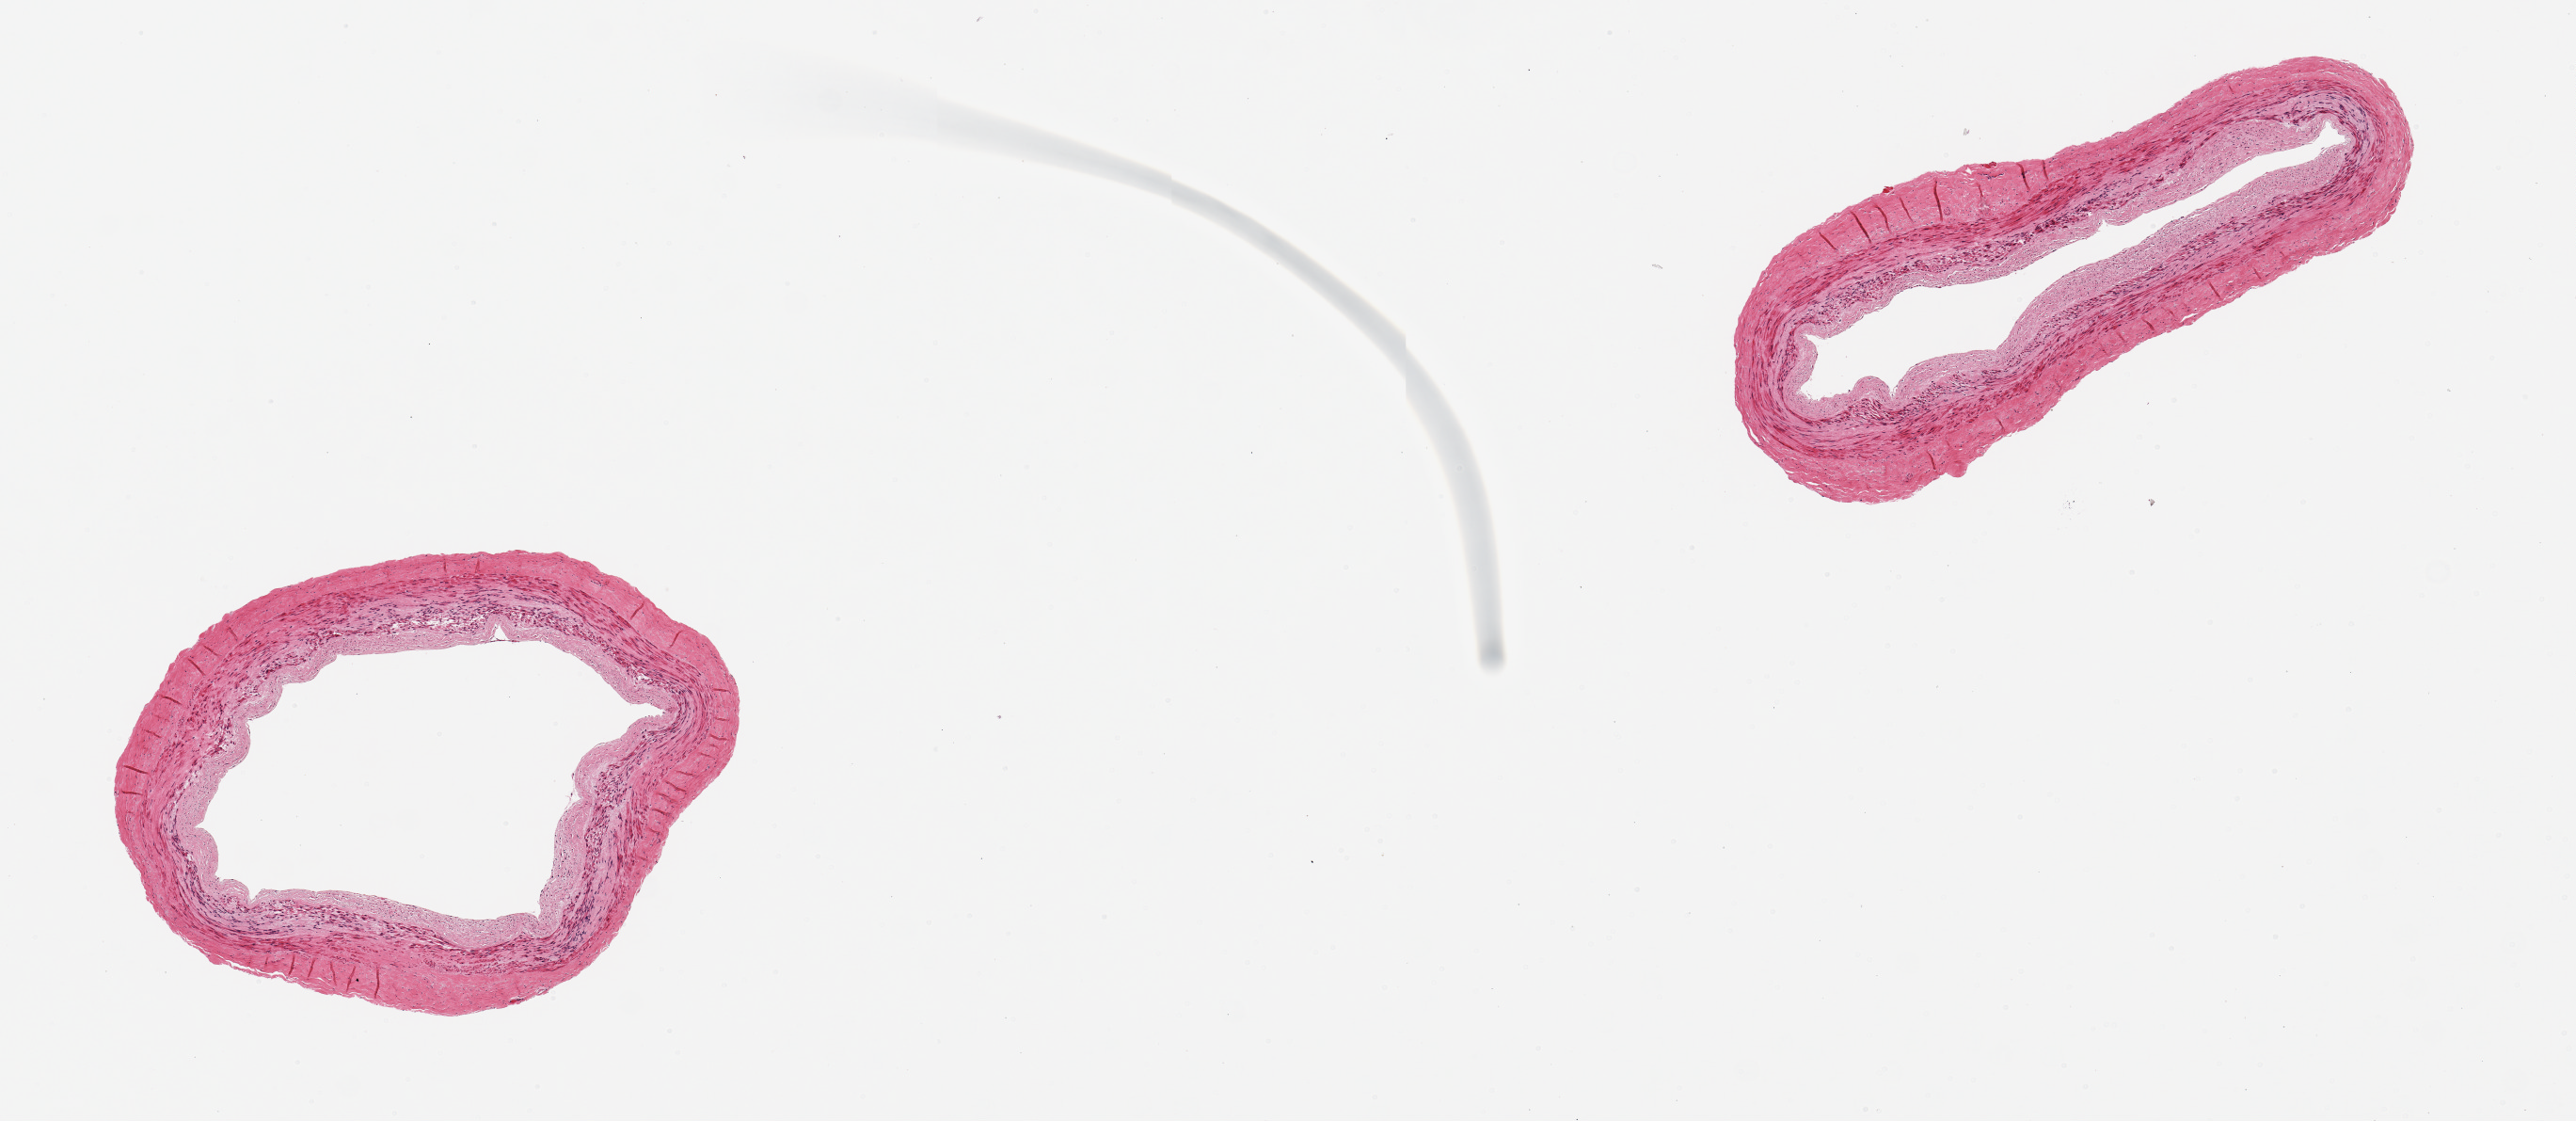
Whole-slide image, haematoxylin and eosin stain — a low-resolution overview of the entire scanned area, about 10.8 x 4.7 mm (slide scanned at 20x), PAXgene-fixed, paraffin-embedded tissue, target tissue: tibial artery, donor tissue sample. Female donor.
• pathologist's review note for this sample: 2 pieces, well trimmed; mild intimal thickening